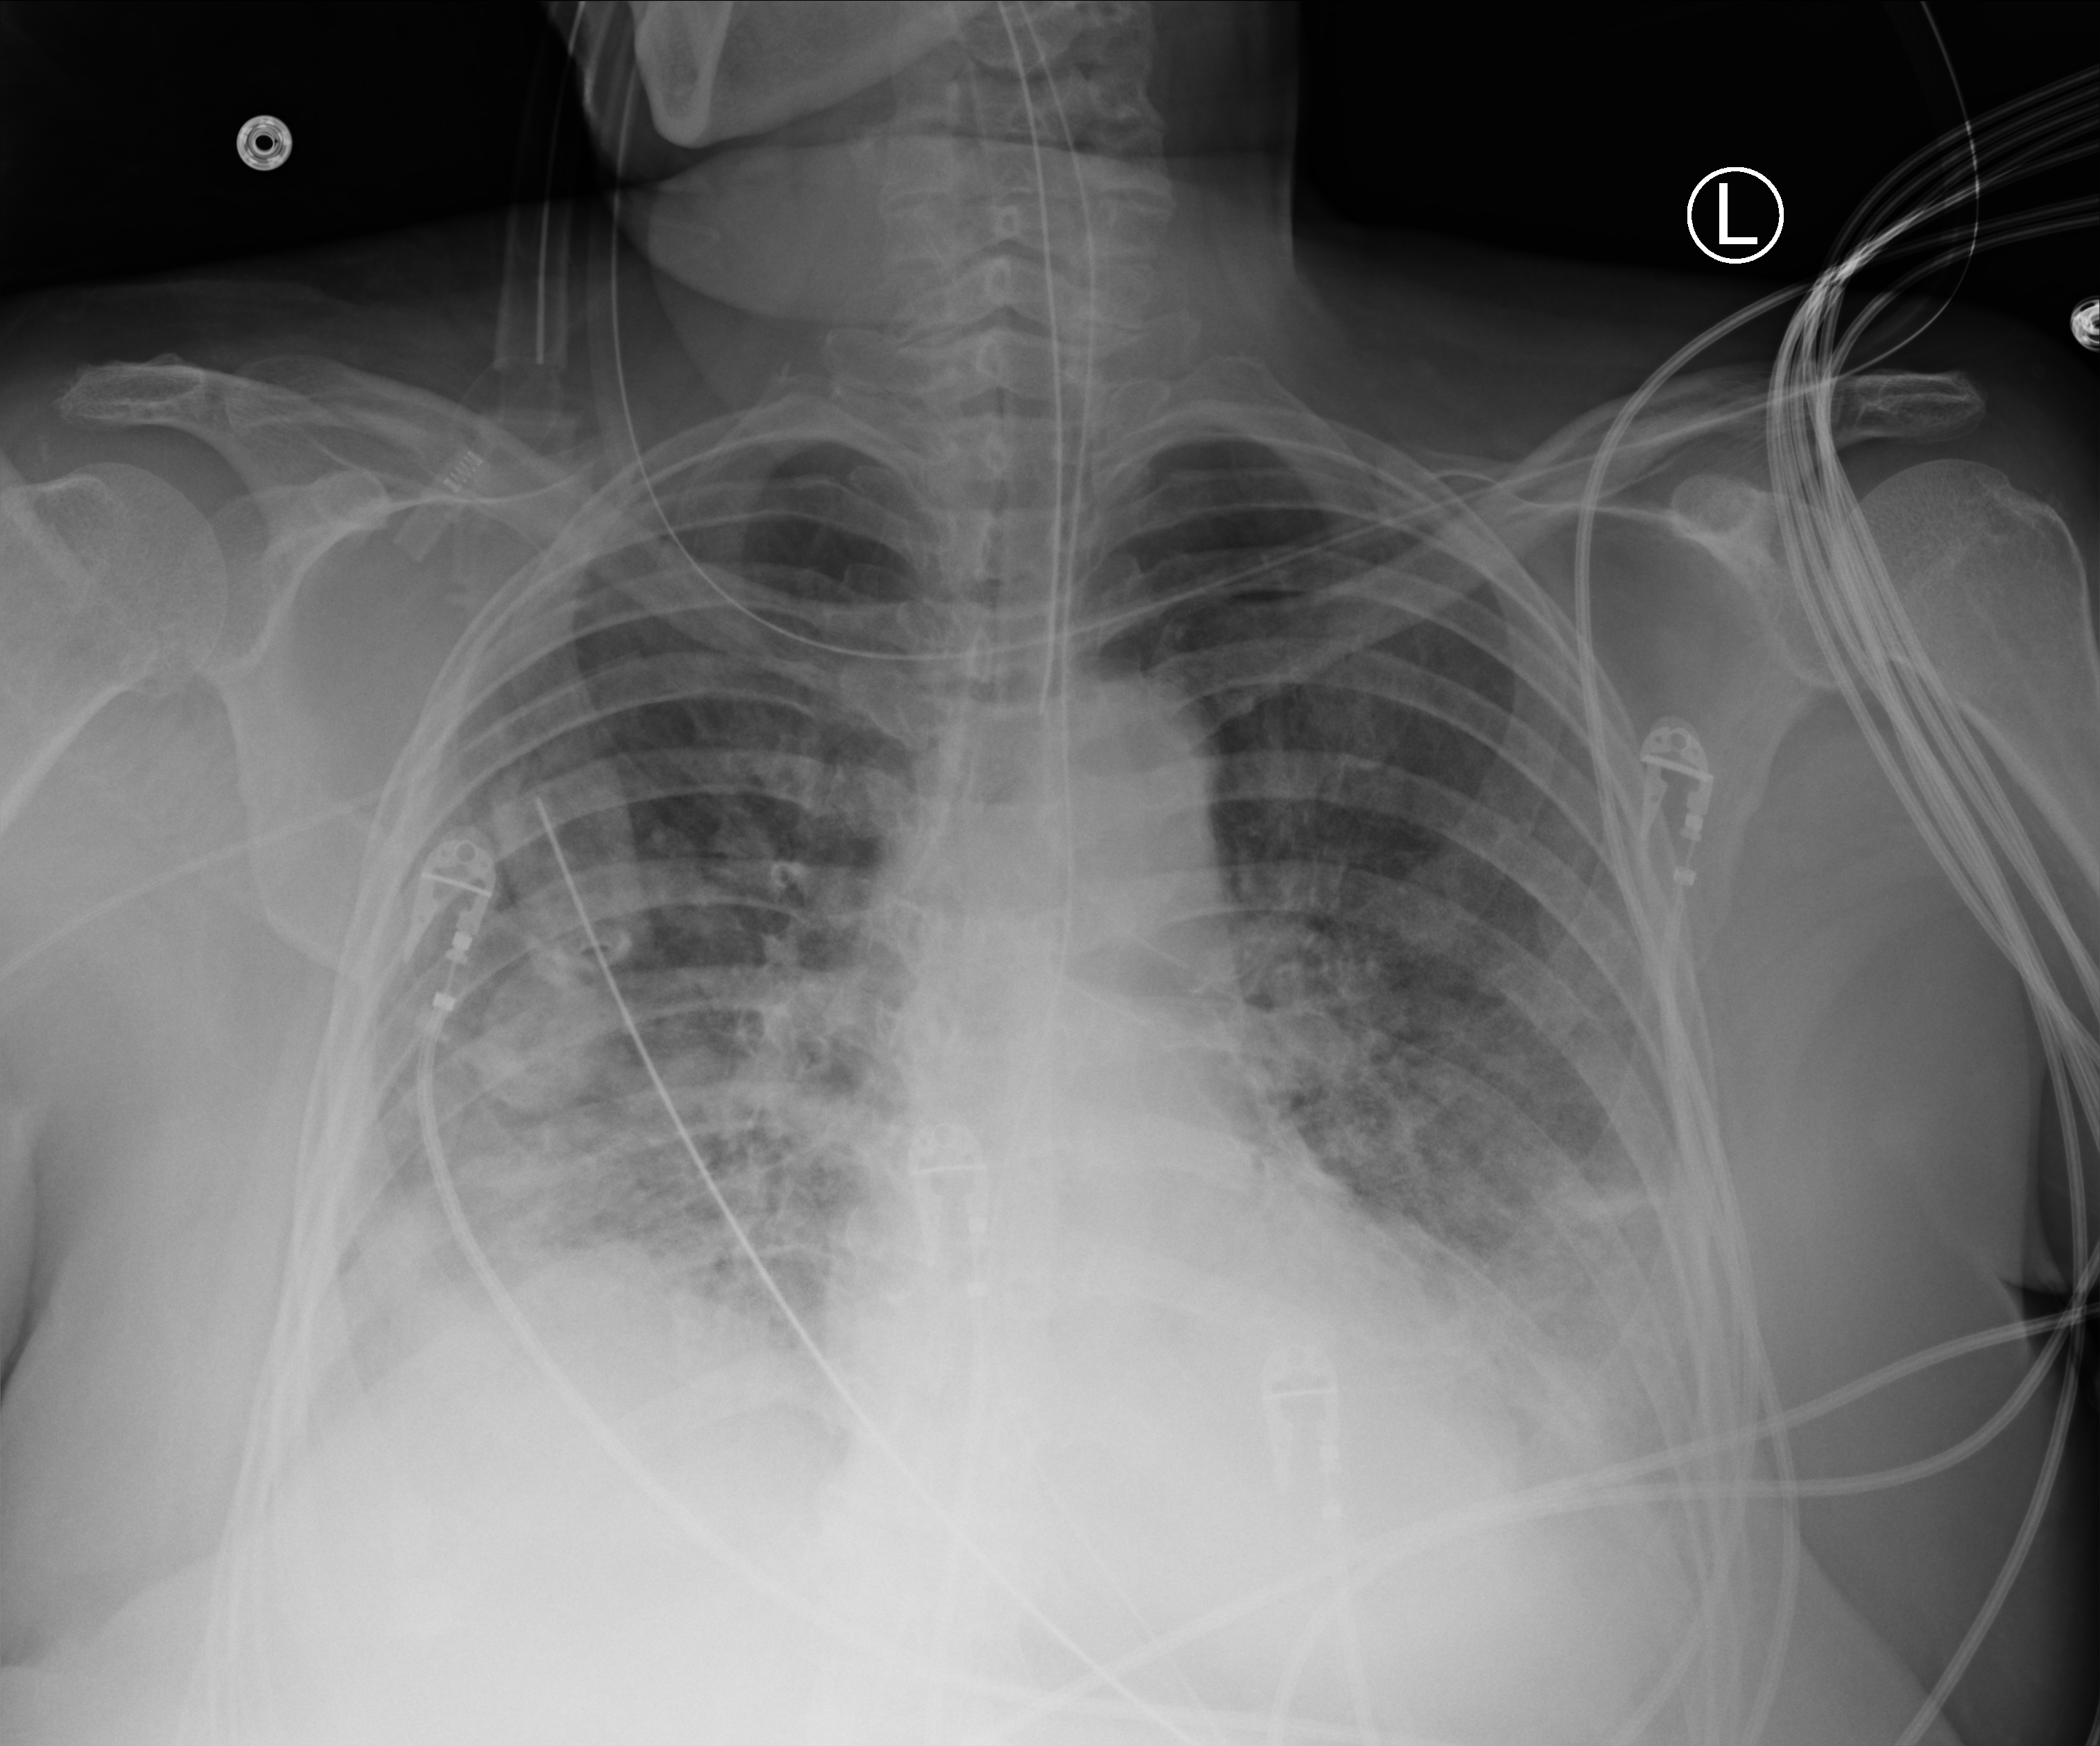
Portable chest radiograph. Female patient hospitalised with COVID-19, age 75–90 years.
Hospital-stay facts (about this admission, not read from this image; timing relative to this image not recorded):
- admitted to intensive care during this hospital stay: yes
- other chronic lung disease (admission record): no
- mechanically ventilated during this hospital stay: yes